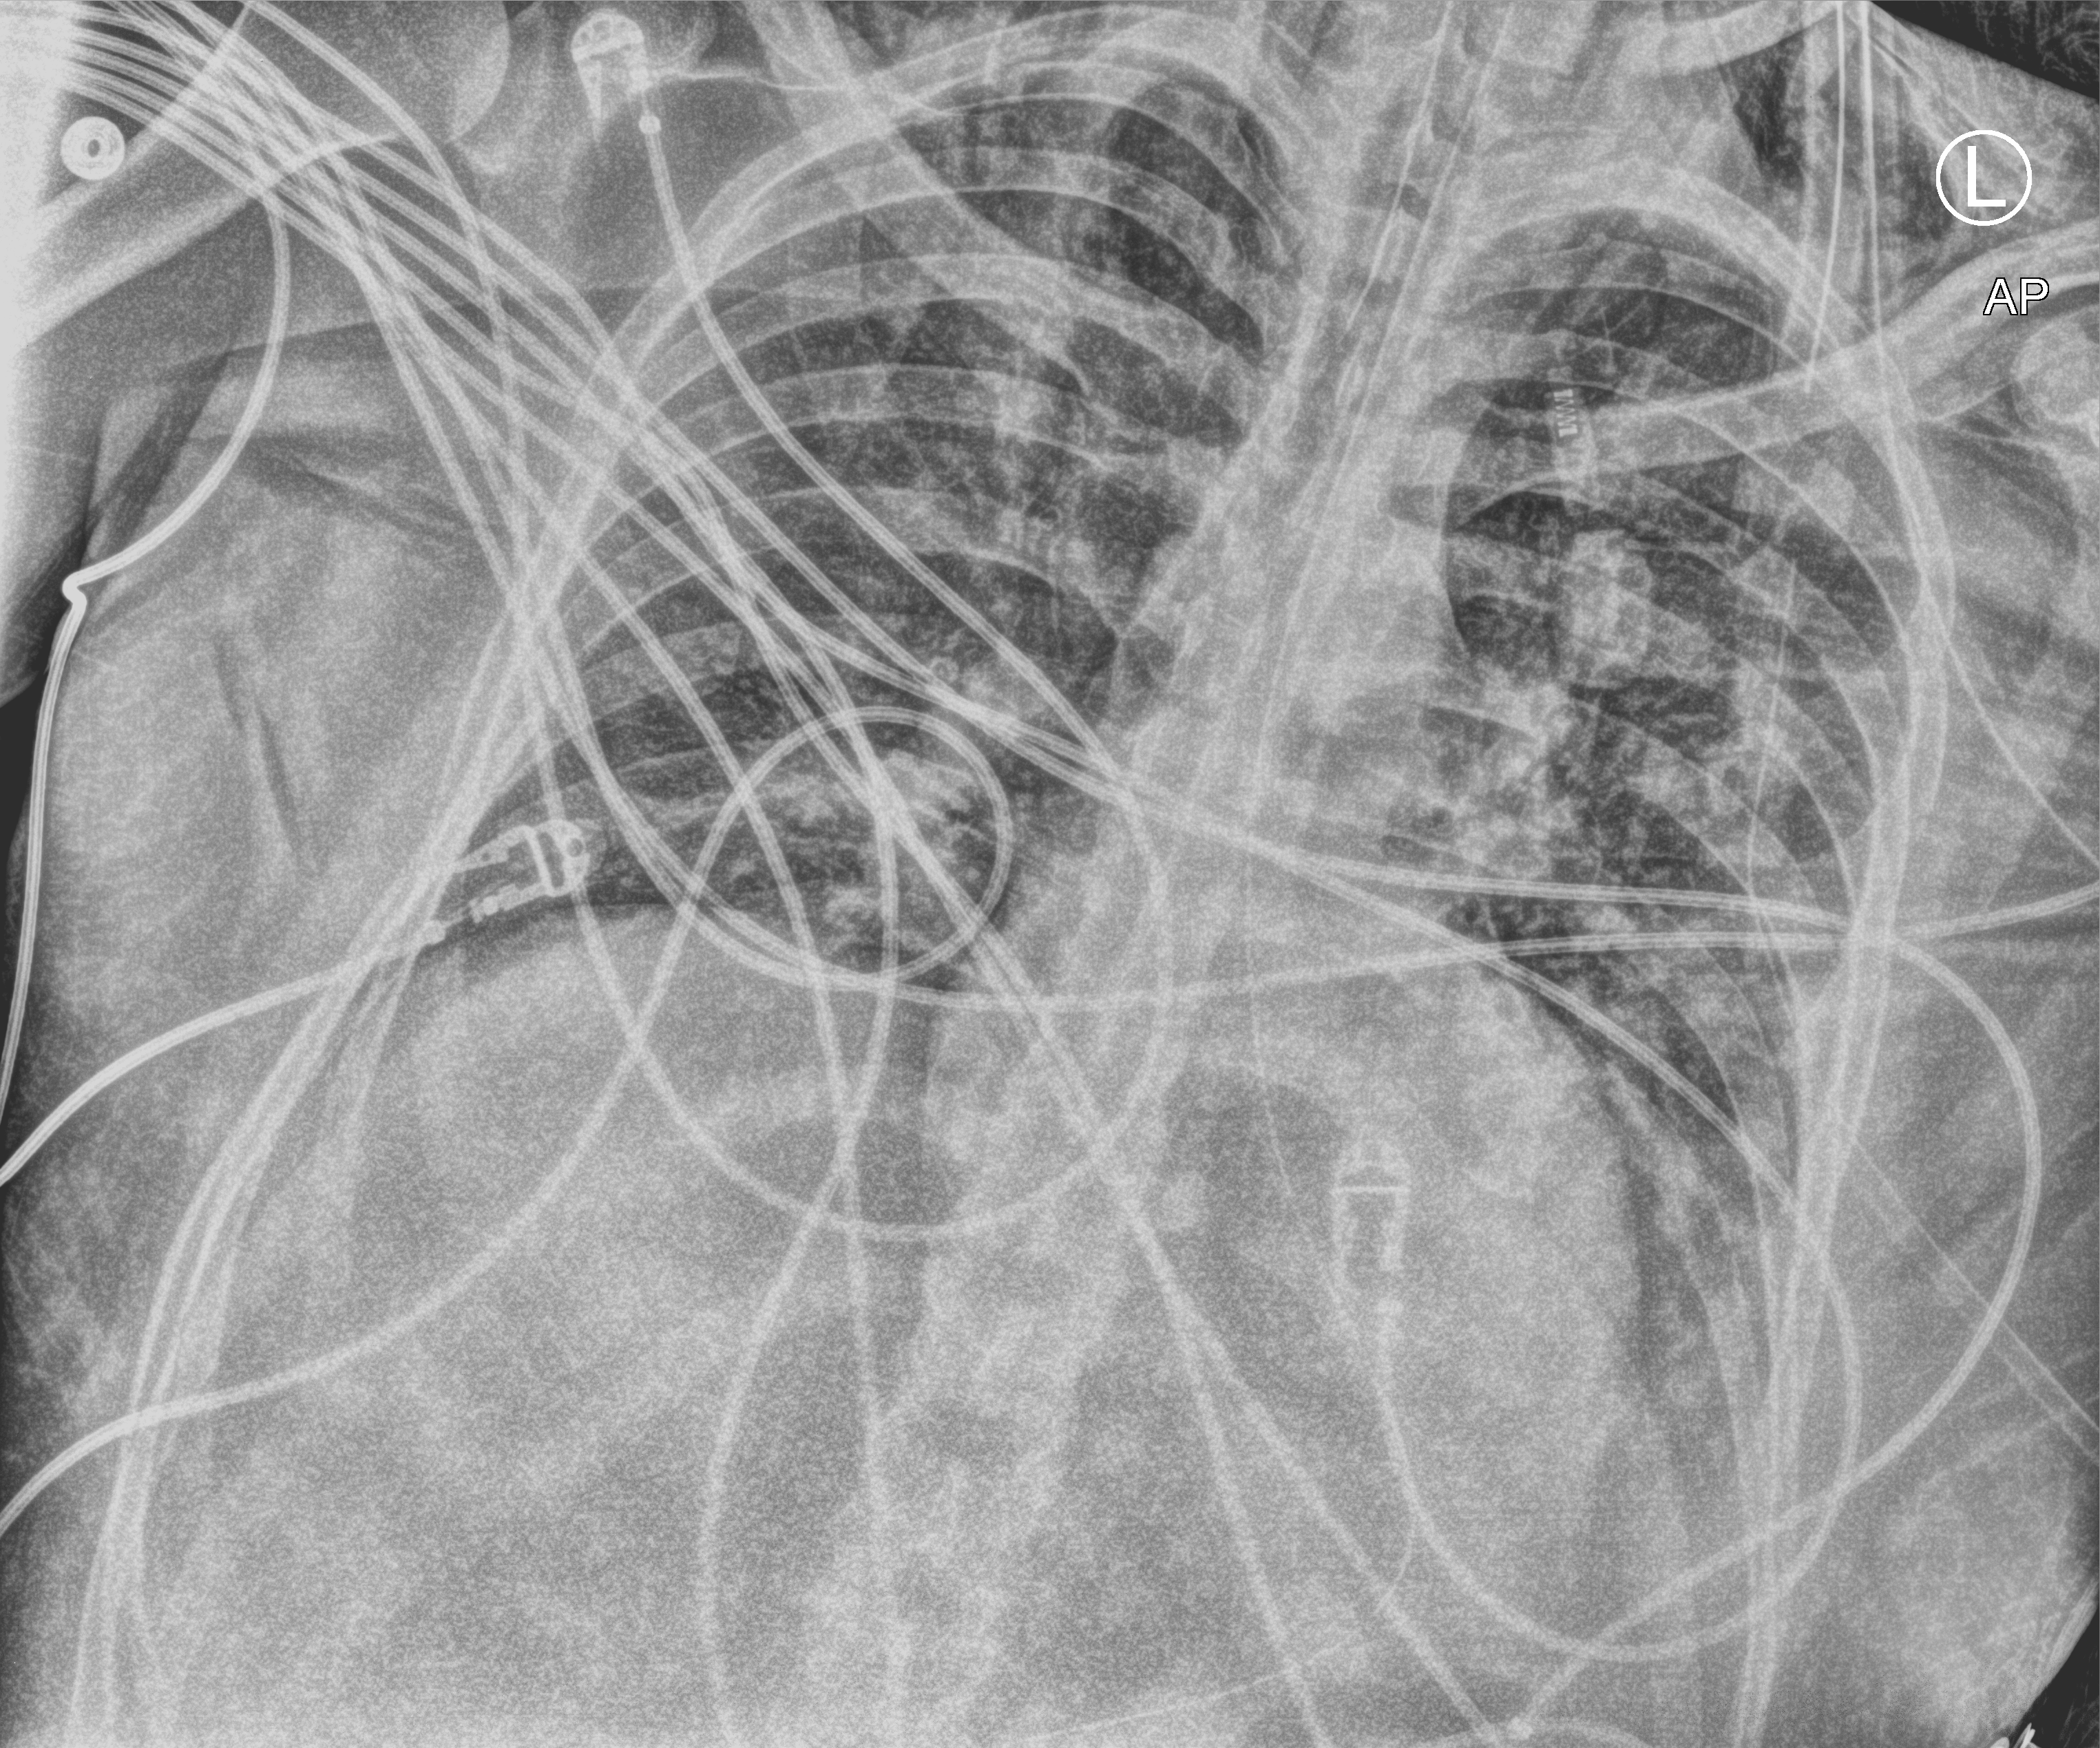
Chest X-ray (portable); anteroposterior (AP) projection. Male patient hospitalised with COVID-19, age 18–59 years.
From the hospital-stay record, not from the radiograph (when in the stay this image was taken is not recorded):
- chronic kidney disease (admission record): no